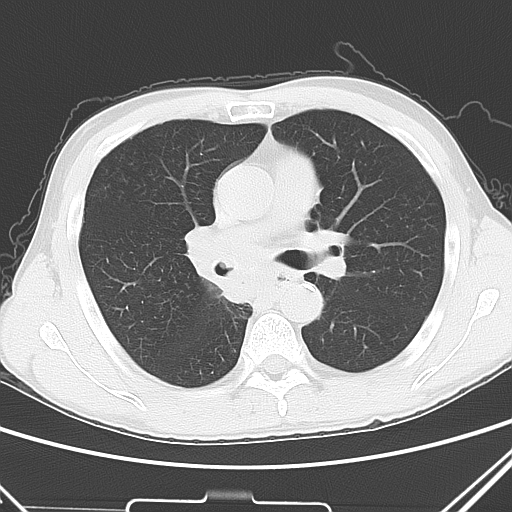
Chest CT, one axial slice. Slice 28 of 51 in the series (ordered by position). Lung window (W 1500 / L -600 HU). 512 × 512 image matrix, field of view 327 × 327 mm. Patient: male, 52 years. Case-level facts recorded for this patient, not image findings: clinical TNM (as recorded): T2a N0 M1c.
Annotated regions visible in this slice (bounding box drawn by a radiologist):
- lung tumour (recorded histology: squamous cell carcinoma): bounding box <178,218,248,317> (left, top, right, bottom; pixels)